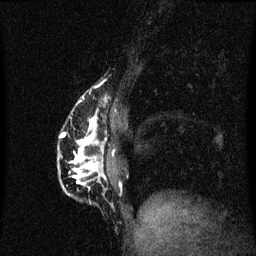
Breast MRI (dynamic contrast-enhanced), one sagittal slice. Position 17 of 60 along the scan axis. Dynamic contrast-enhanced series, image 2 of 3 at this slice position (ordered by acquisition). 1.5 T. TE 4.2 ms, TR 8.4 ms. 2 mm slice thickness. 256 × 256 image matrix, field of view 200 × 200 mm. Patient: female, 40 years.
Outlined on this slice (semi-automatic segmentation, software-assisted and operator-edited):
- analysis volume of interest (the breast-tissue region the enhancement analysis was run in; not a lesion): box from (x=58, y=88) to (x=111, y=199) px
- tumour enhancement mask (voxels above the 70 % enhancement threshold inside the analysis volume of interest): (x=60, y=114)–(x=107, y=187)